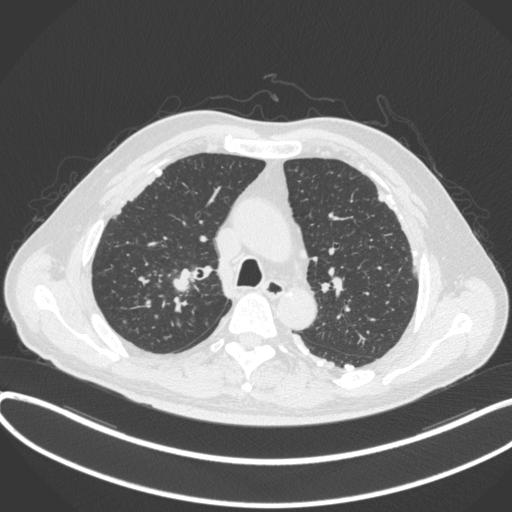
Chest CT, one axial slice. Slice 295 of 455 in the series (ordered by position). Reconstruction kernel B31f. 120 kVp. Lung window (W 1500 / L -600 HU). 1 mm slice thickness. 512 × 512 image matrix. Male patient, age 58 years. From the clinical record (not read from this slice): clinical TNM (as recorded): T1c N0 M0.
Outlined on this slice (bounding box drawn by a radiologist):
- lung tumour (recorded histology: squamous cell carcinoma): bounding box <168,266,201,298> (left, top, right, bottom; pixels)